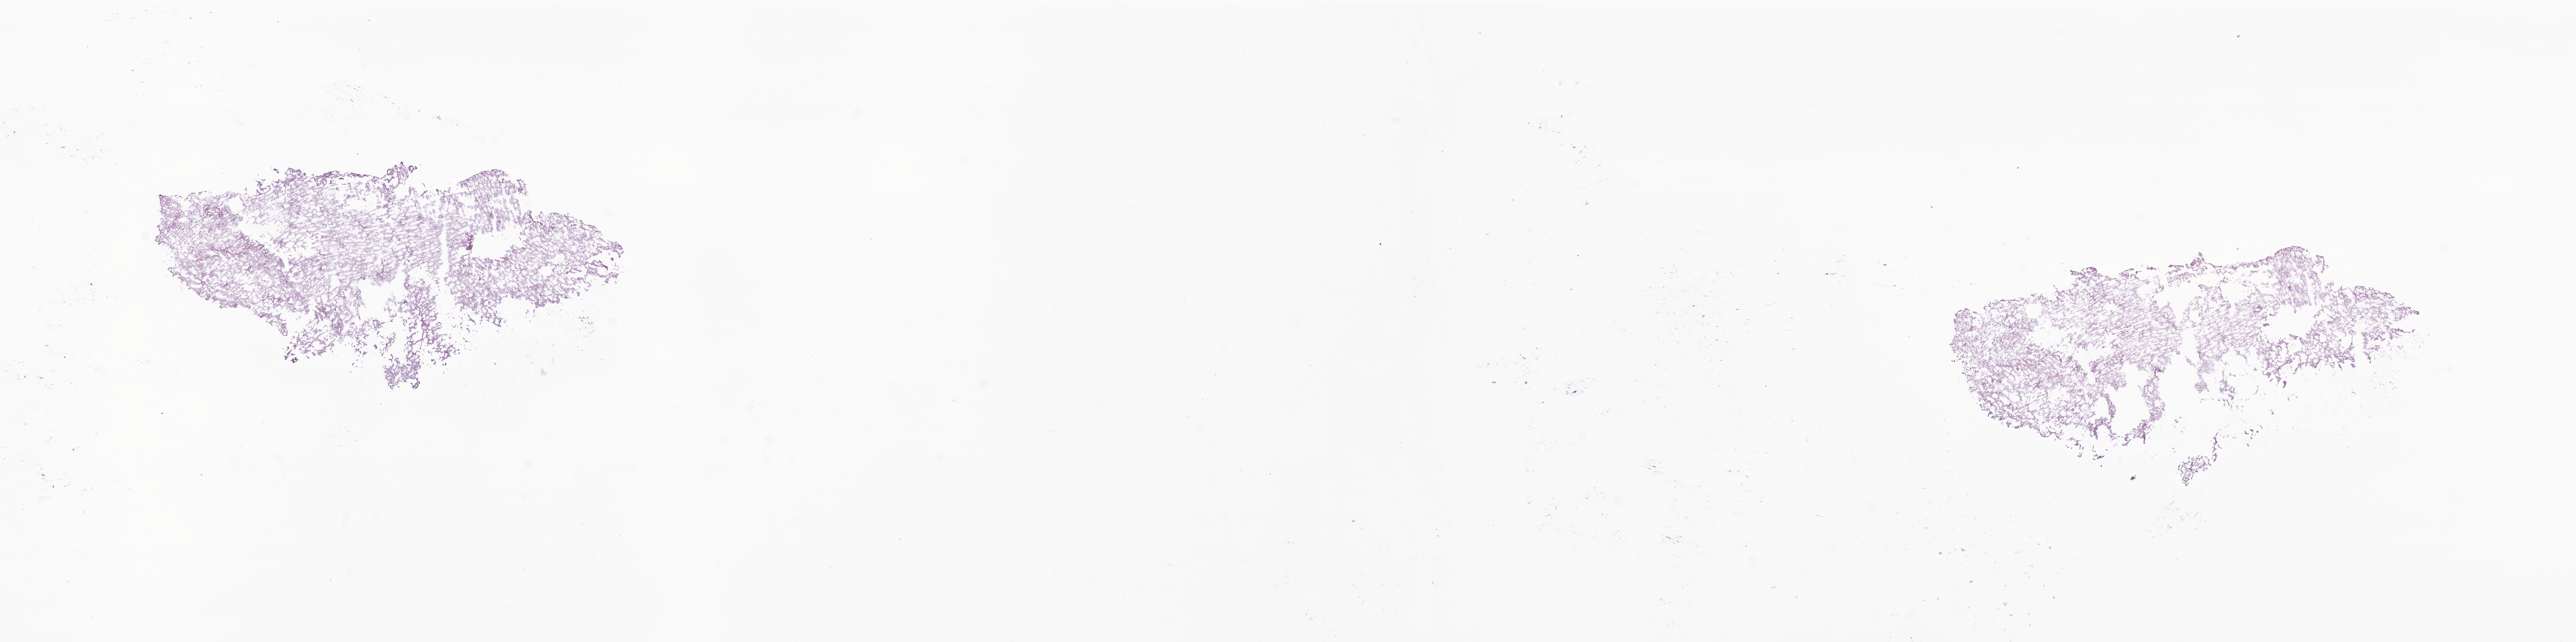
H&E whole-slide image of tumor tissue from the brain, whole scanned area (about 31.2 x 7.8 mm) shown as a low-resolution overview; frozen section (OCT-embedded). Male patient, age 43 months (3 years 7 months).
Diagnosis: Neoplasm, uncertain whether benign or malignant.